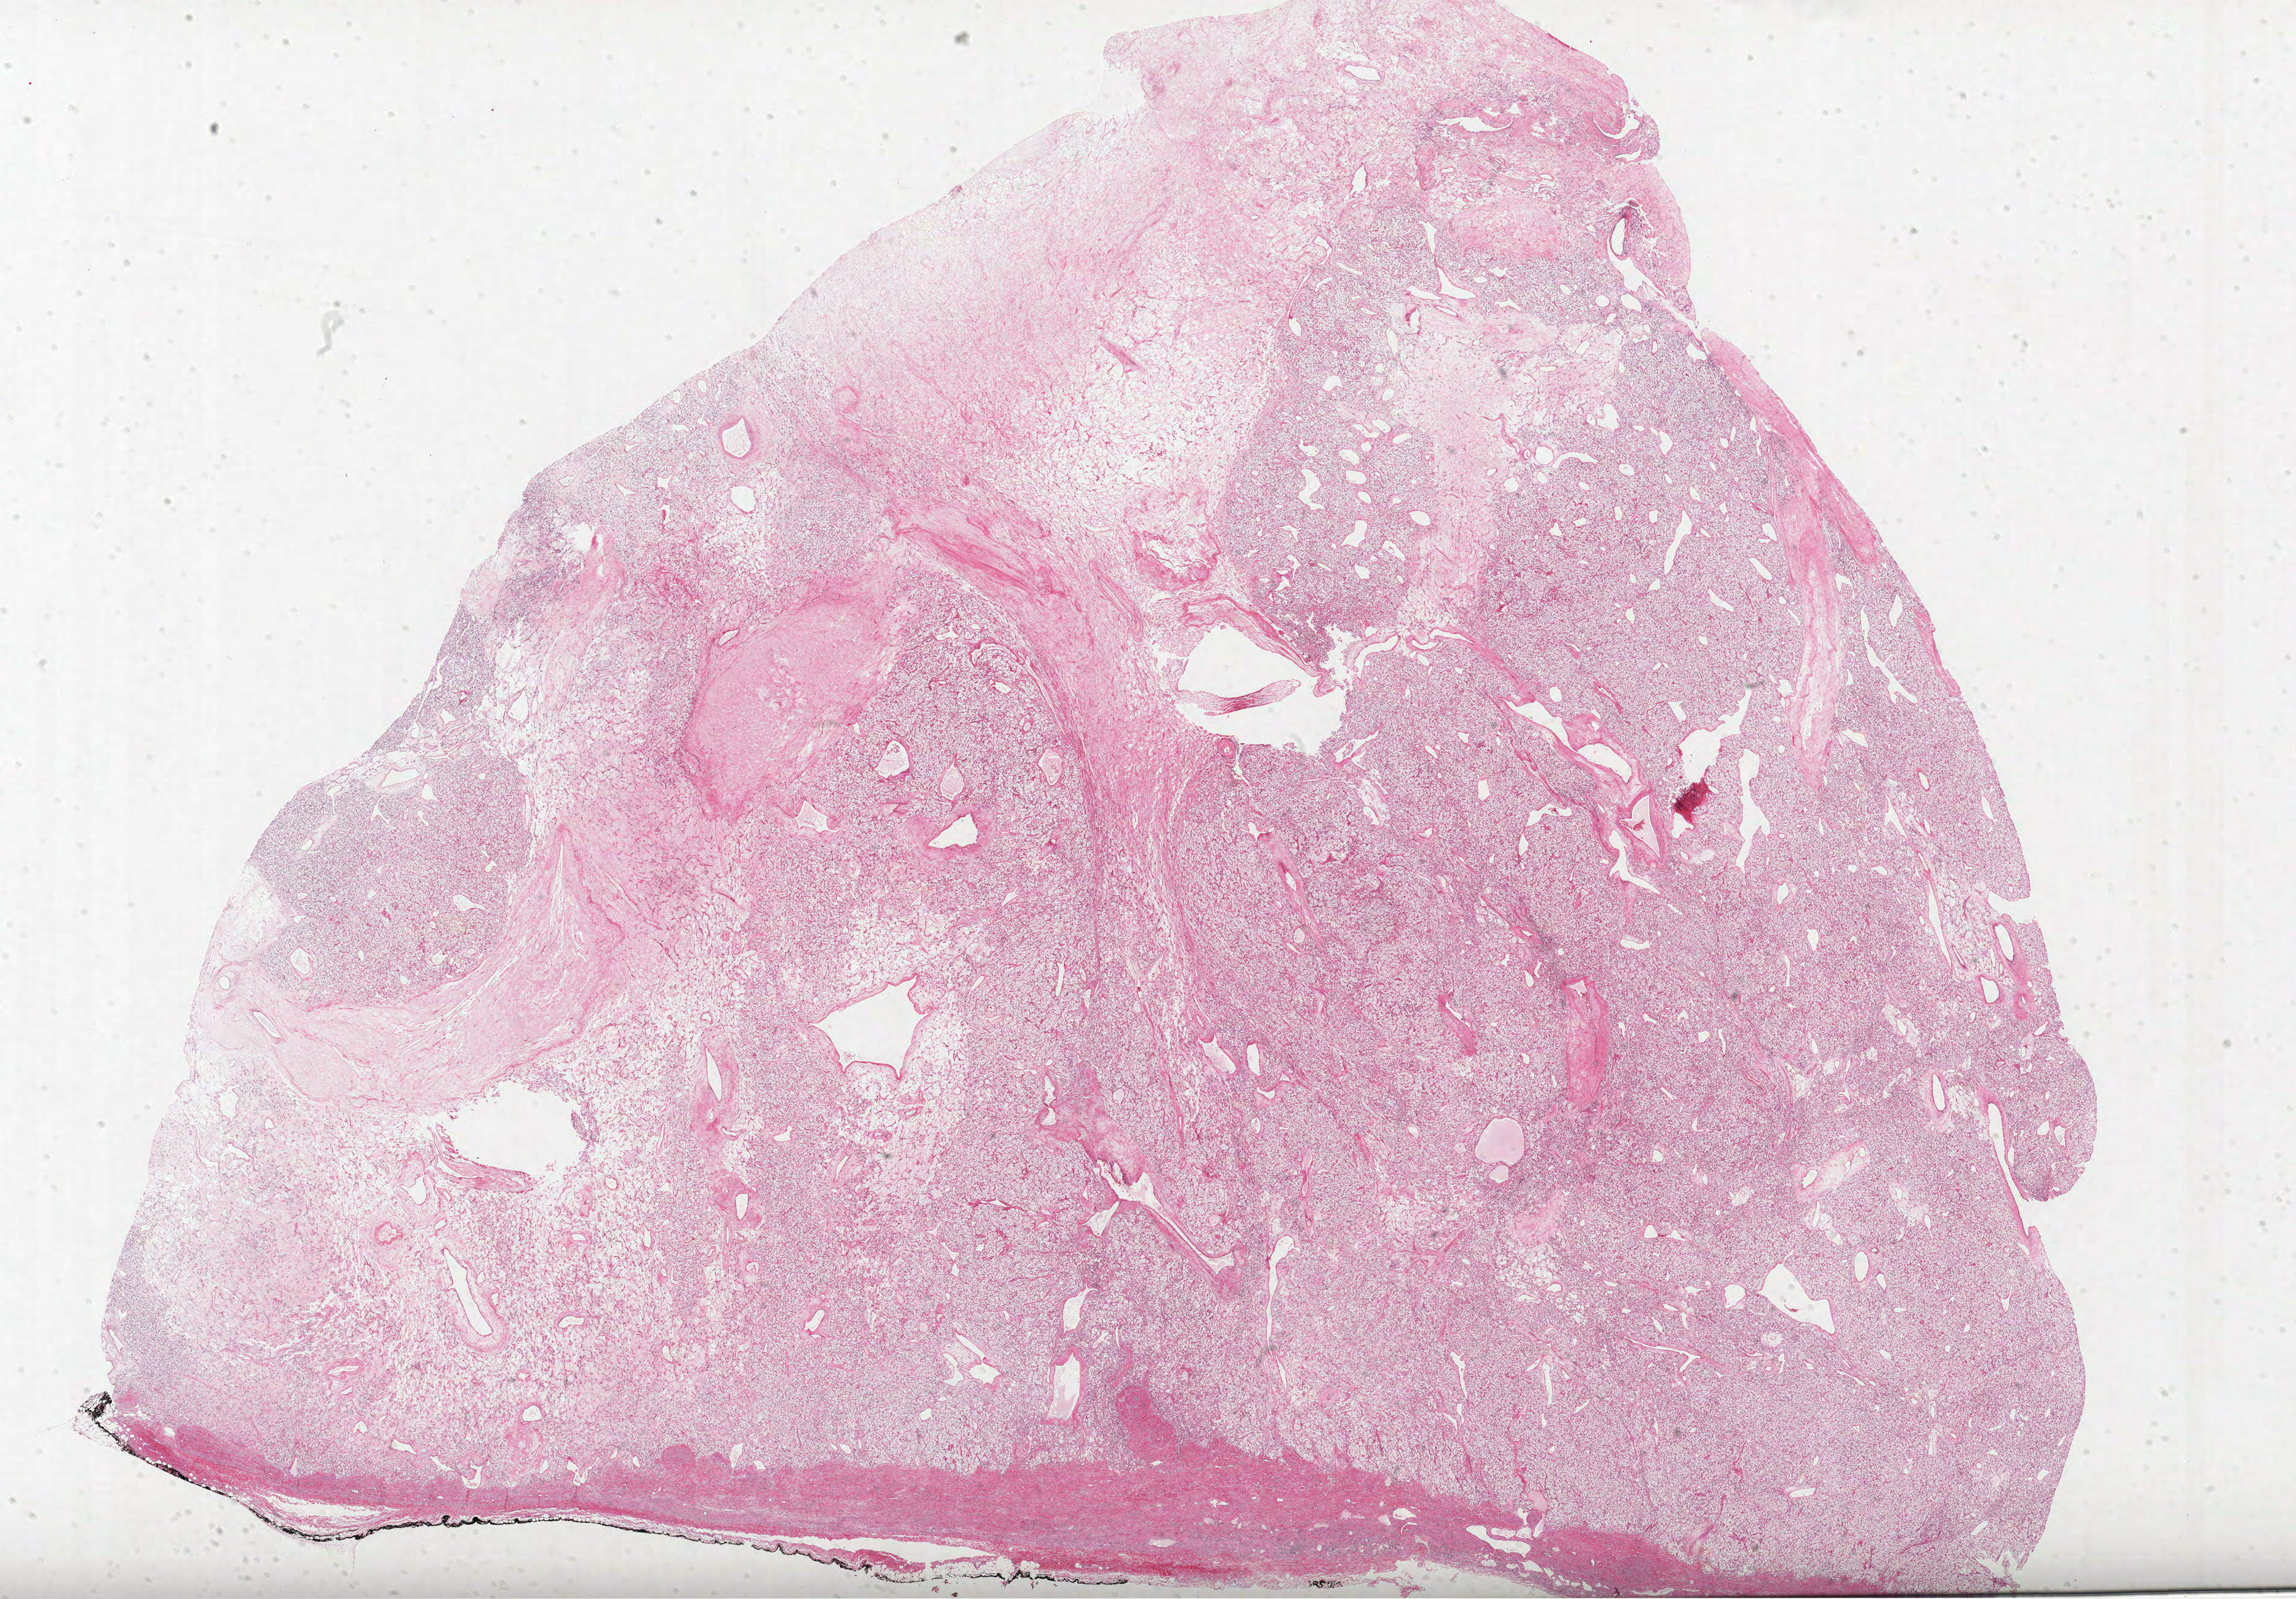
Whole-slide histology image, H&E-stained — shown as a low-resolution overview of the whole scanned area (about 30.2 x 21.0 mm). FFPE section. Primary tumour sample from the kidney. Female patient; age at initial diagnosis 76 years. Histologic grade: G2 (moderately differentiated).
- diagnosis: Clear cell adenocarcinoma, NOS
- lymph nodes positive (case pathology): 0 of 2 examined
- AJCC pathologic stage: II